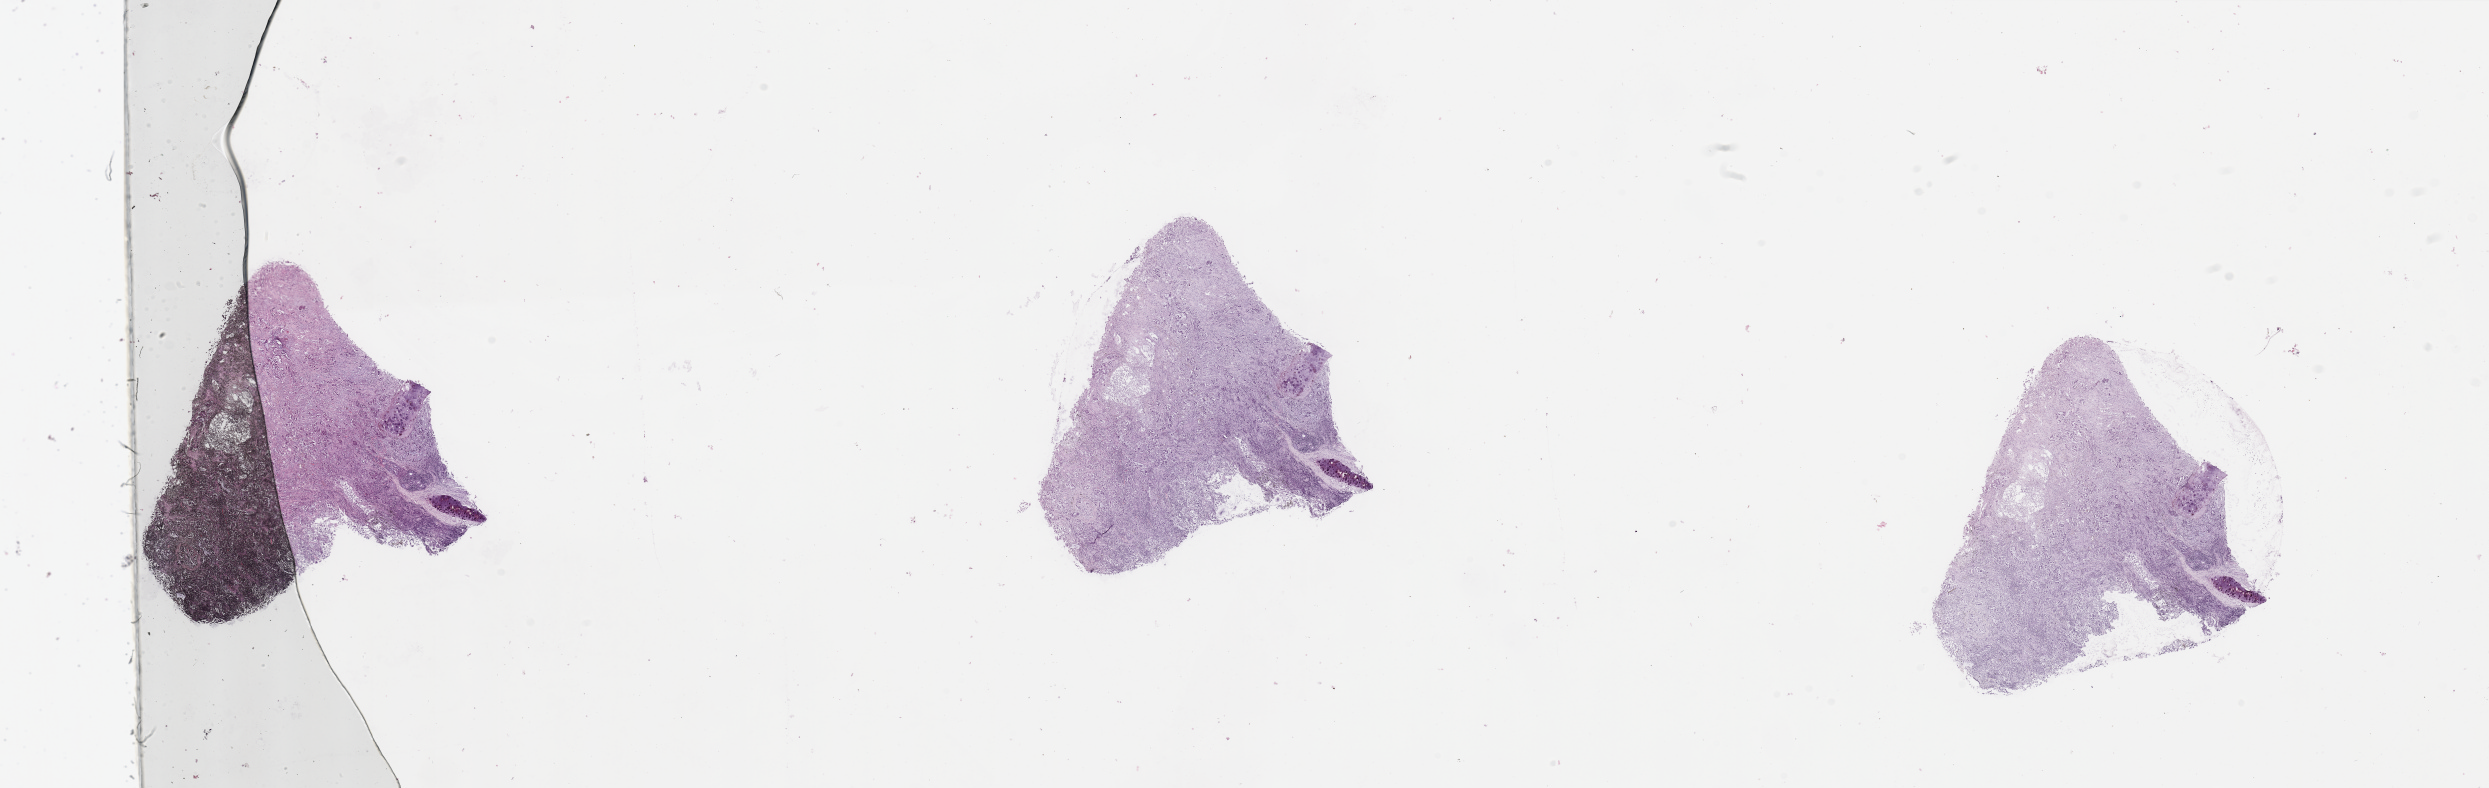
Whole-slide histology image, H&E, low-resolution overview of the scanned area, about 39.4 x 12.5 mm; tumour tissue sample, sampled site: lung. Male, 76 y/o. Histologic grade: G2 (moderately differentiated). Slide review estimates, as recorded: tumour nuclei 75%, necrosis 10%.
AJCC pathologic stage: IIA. Diagnosis: Adenocarcinoma, NOS.